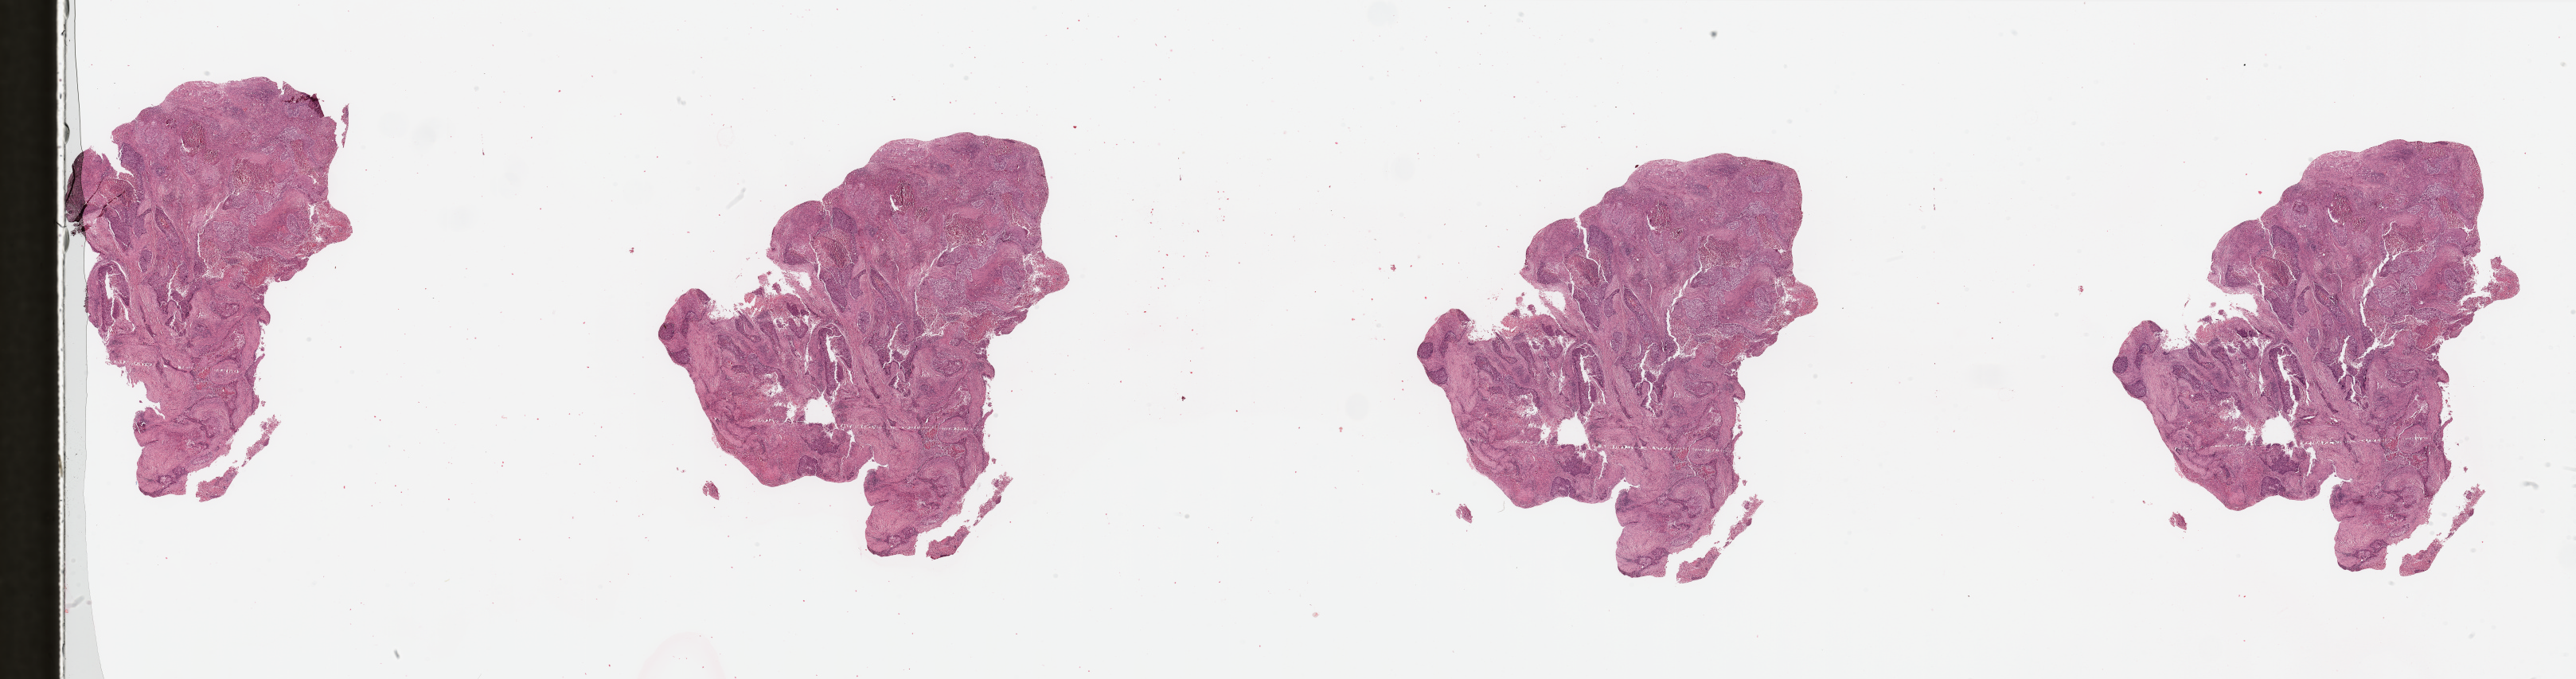
Whole-slide histology image, H&E, a low-resolution overview of the entire scanned area, about 51.2 x 13.5 mm (slide scanned at 20x); head and neck, tissue type not recorded. Patient: male, age 64 years.
- patient diagnosis: Squamous cell carcinoma, NOS (larynx, NOS)